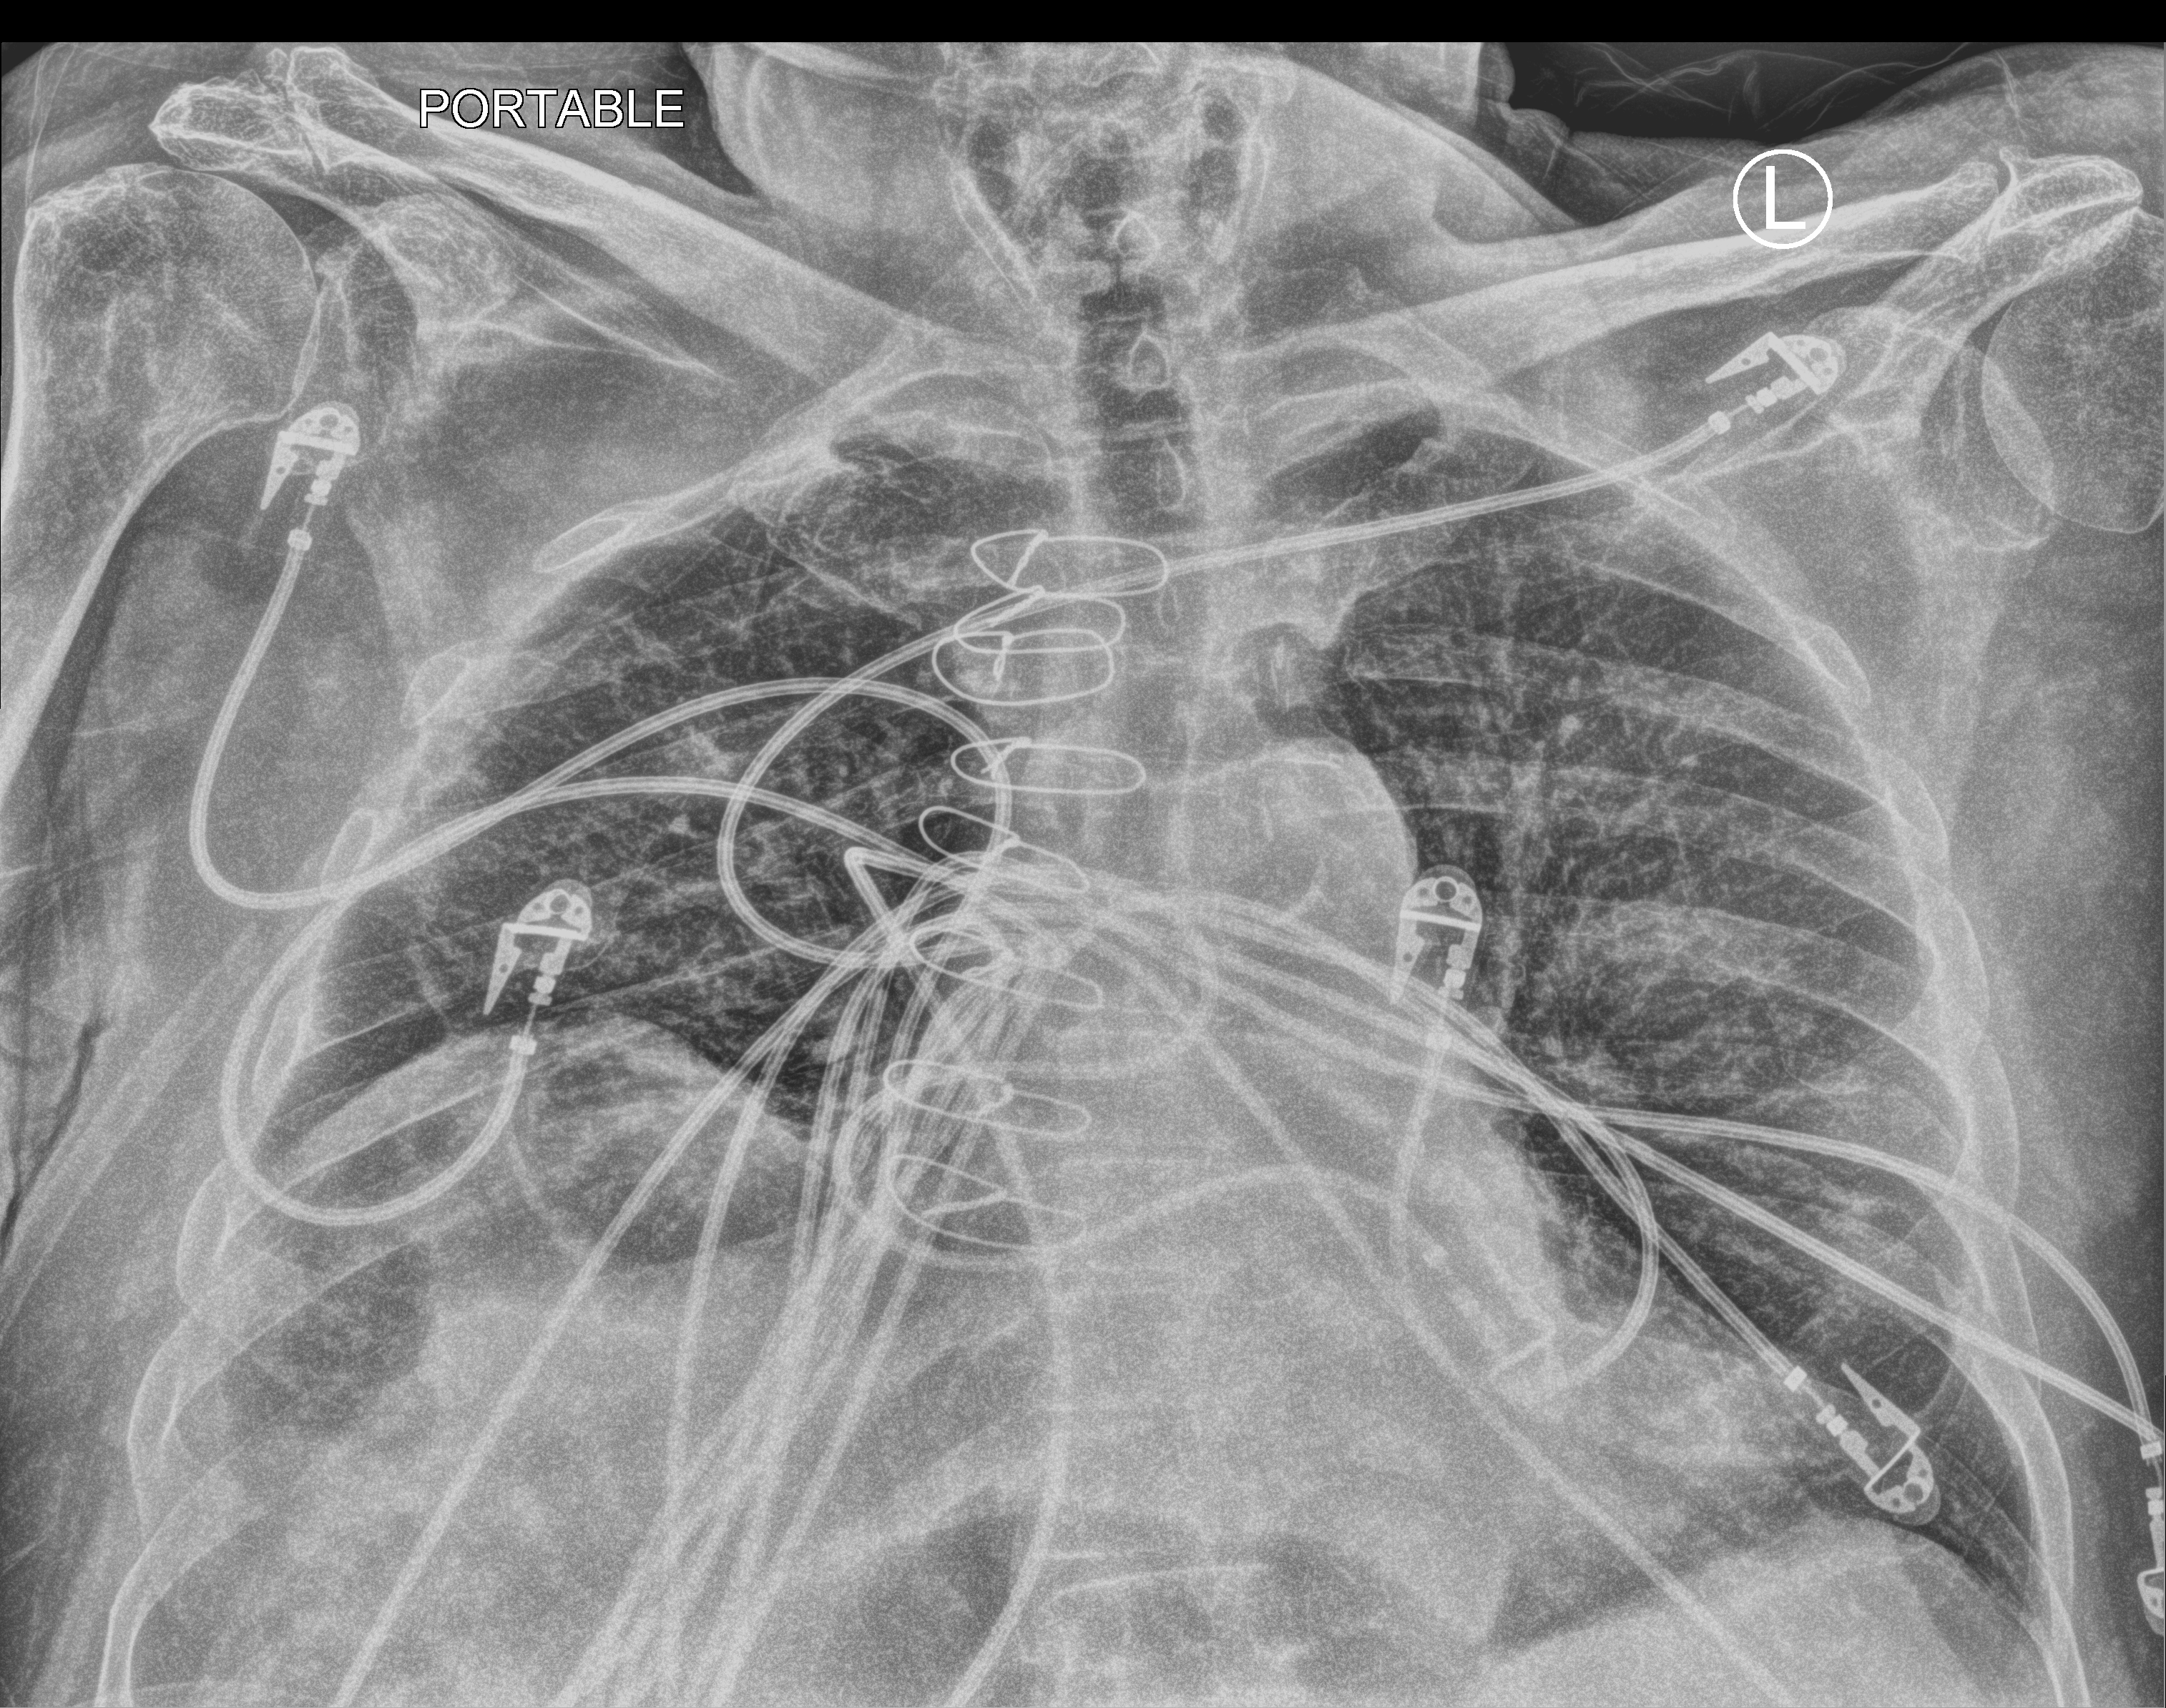
Portable chest radiograph, anteroposterior (AP) projection. Patient hospitalised with COVID-19; male, aged 75–90 years.
From the hospital-stay record, not from the radiograph (when in the stay this image was taken is not recorded): mechanically ventilated during this hospital stay: no; admitted to intensive care during this hospital stay: no.